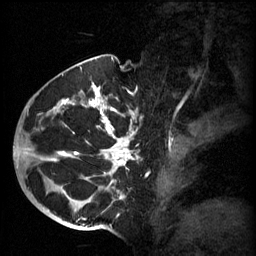
Breast MRI (dynamic contrast-enhanced), one sagittal slice; slice 40 of 60 in the series (ordered by position); 3 images stored at this slice position (order not interpretable as contrast timing); 1.5 T; TE 4.2 ms, TR 11 ms; 256 × 256 image matrix. Patient: female, 51 years.
Annotated regions visible in this slice (semi-automatically segmented with operator editing):
- analysis volume of interest (the breast-tissue region the enhancement analysis was run in; not a lesion): box from (x=48, y=82) to (x=161, y=197) px
- tumour enhancement mask (voxels above the 70 % enhancement threshold inside the analysis volume of interest): (x=56, y=82)–(x=138, y=197)